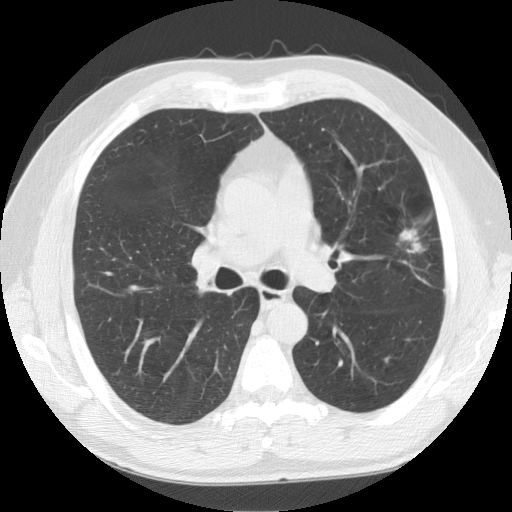
Axial slice from a low-dose chest CT screening exam, baseline annual screen, lung window (W 1500 / L -600 HU), 2.5 mm slice thickness, slice 52 of 141 in the series. Male participant, aged 59 years at enrolment. Former smoker at enrolment.
Expert-annotated lung lesion, bounding box <378,203,459,284> (left, top, right, bottom; pixels). Reader record for this screening exam (exam-level; its link to the box is not recorded): non-calcified nodule or mass ≥4 mm, left upper lobe, 23 × 23 mm, spiculated (stellate) margins, soft tissue attenuation. Official screen result: positive, change unspecified: nodule(s) >= 4 mm or enlarging nodule(s), mass(es), or other non-specific abnormalities suspicious for lung cancer. Lung cancer was diagnosed 28 days after this screen: squamous cell carcinoma, NOS, left upper lobe, moderately differentiated (G2), stage IA (AJCC 6th edition), 27 mm at pathology.